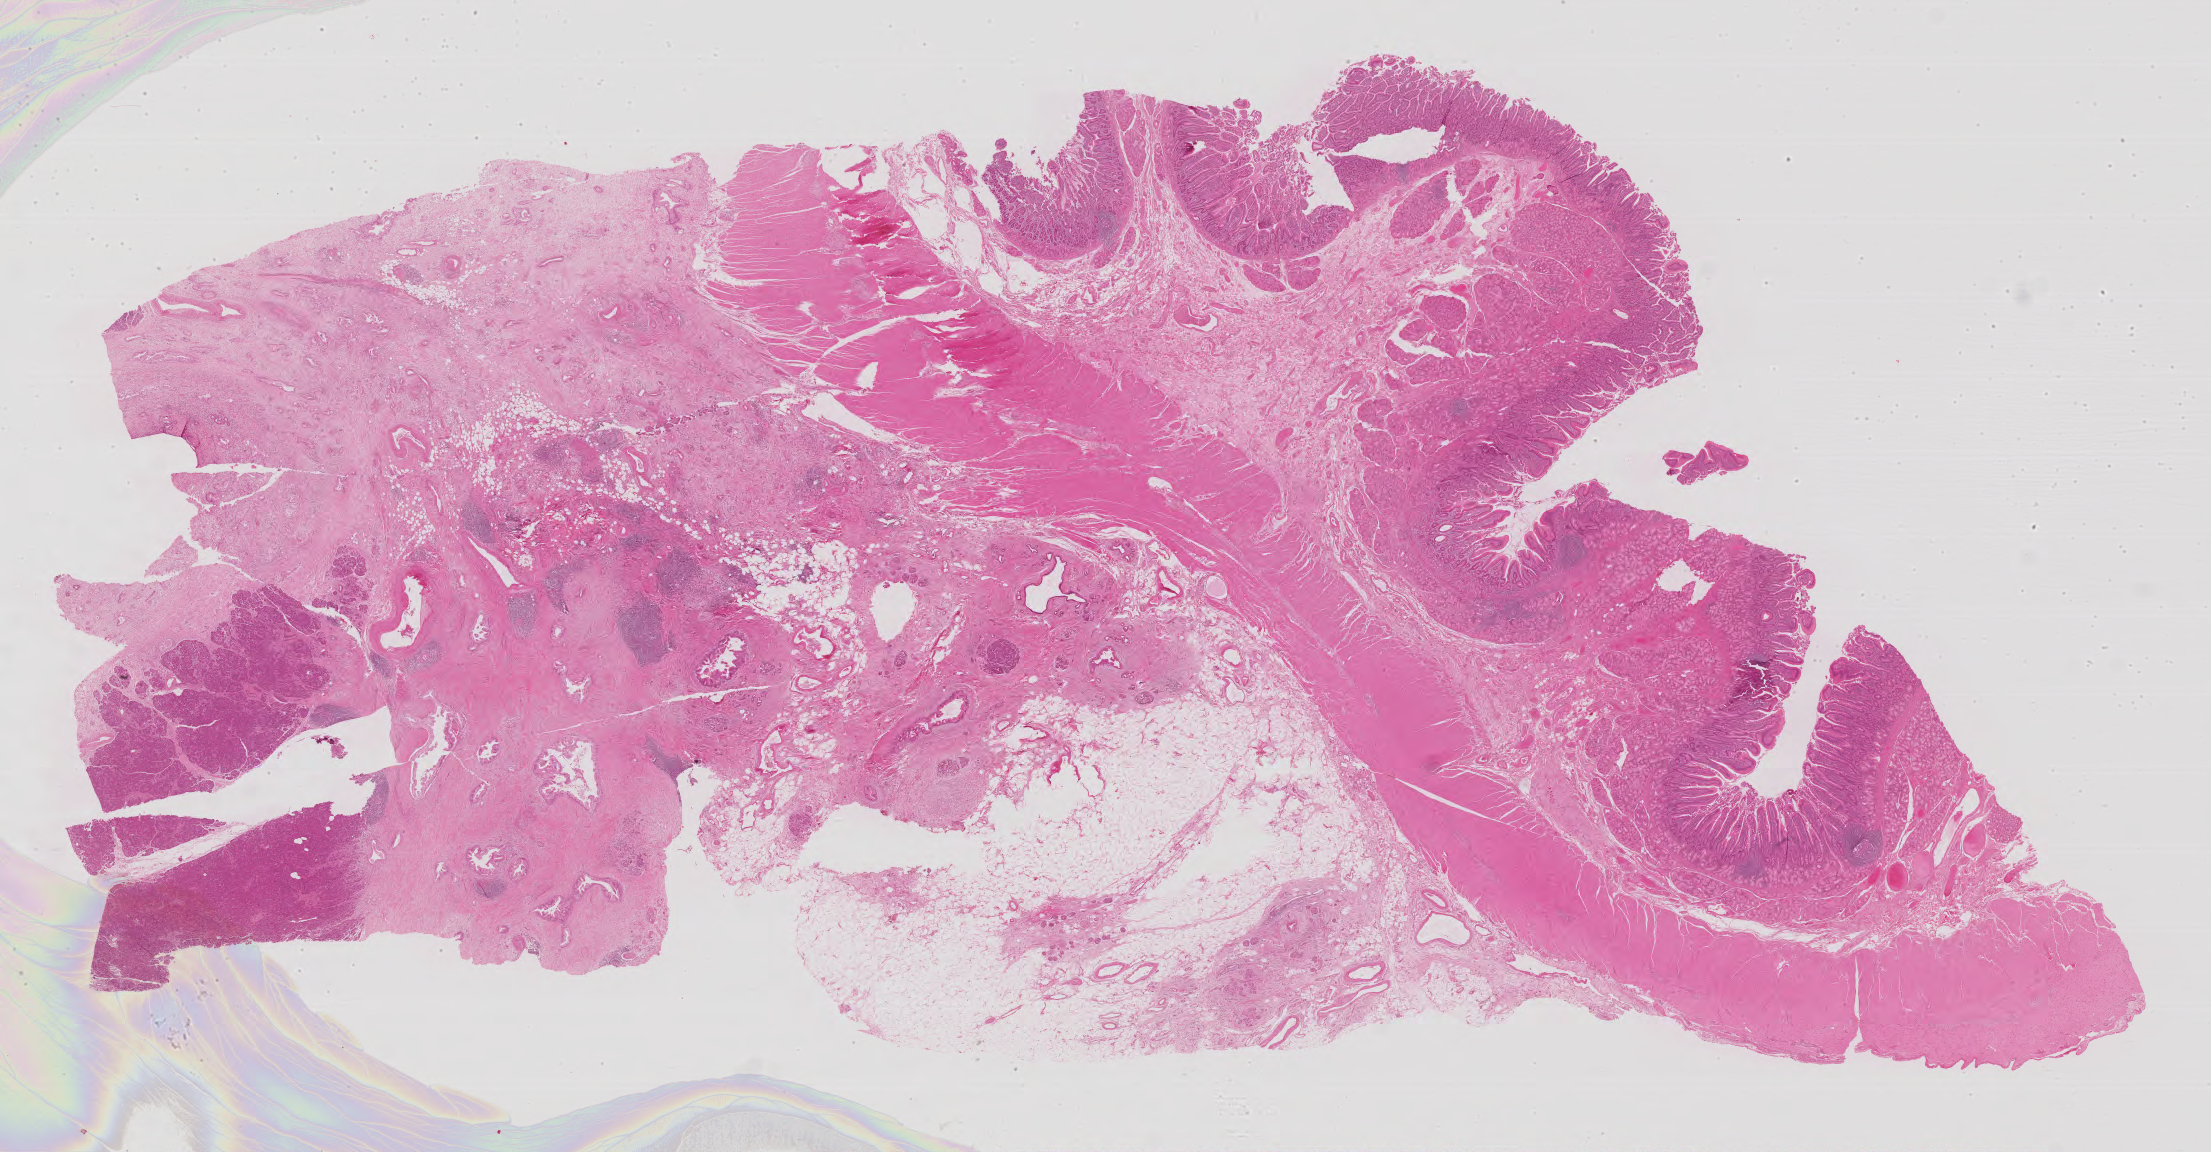
Whole-slide histology image, H&E, a low-resolution overview of the entire scanned area, about 35.4 x 18.4 mm; FFPE section; pancreas, primary tumour sample. Patient: male, age at initial diagnosis 71 years. Histologic grade: G2 (moderately differentiated).
• AJCC pathologic stage: IIA
• diagnosis: Infiltrating duct carcinoma, NOS (head of pancreas)
• lymph nodes positive (case pathology): 0 of 10 examined